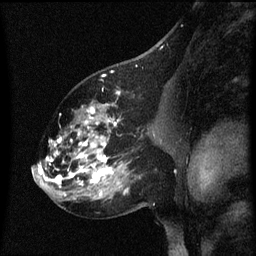
Breast MRI (dynamic contrast-enhanced), one sagittal slice. Position 34 of 60 along the scan axis. Dynamic contrast-enhanced series, image 2 of 3 at this slice position (ordered by acquisition). 1.5 T. TE 4.2 ms, TR 8 ms. 256 × 256 image matrix. Female patient, age 60 years.
Structures marked on this image (semi-automatically segmented with operator editing):
- analysis volume of interest (the breast-tissue region the enhancement analysis was run in; not a lesion): bounding box (x1, y1, x2, y2) in pixels: (49, 102, 158, 197)
- tumour enhancement mask (voxels above the 70 % enhancement threshold inside the analysis volume of interest): (49, 104, 126, 197)